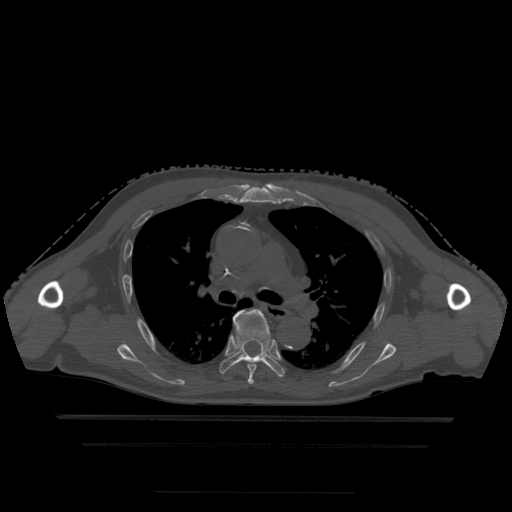
CT including the spine, one axial slice; slice 325 of 522 in the series (ordered by position); bone window (W 1800 / L 400 HU); 1.25 mm slice thickness; 512 × 512 image matrix. Patient age 68 years. From the clinical record (not read from this slice): primary cancer: urothelial.
Annotated regions visible in this slice (semi-automatic segmentation, software-assisted and operator-edited):
- T5 vertebra: box from (x=233, y=309) to (x=265, y=385) px
- T6 vertebra: (x=219, y=313)–(x=285, y=378)